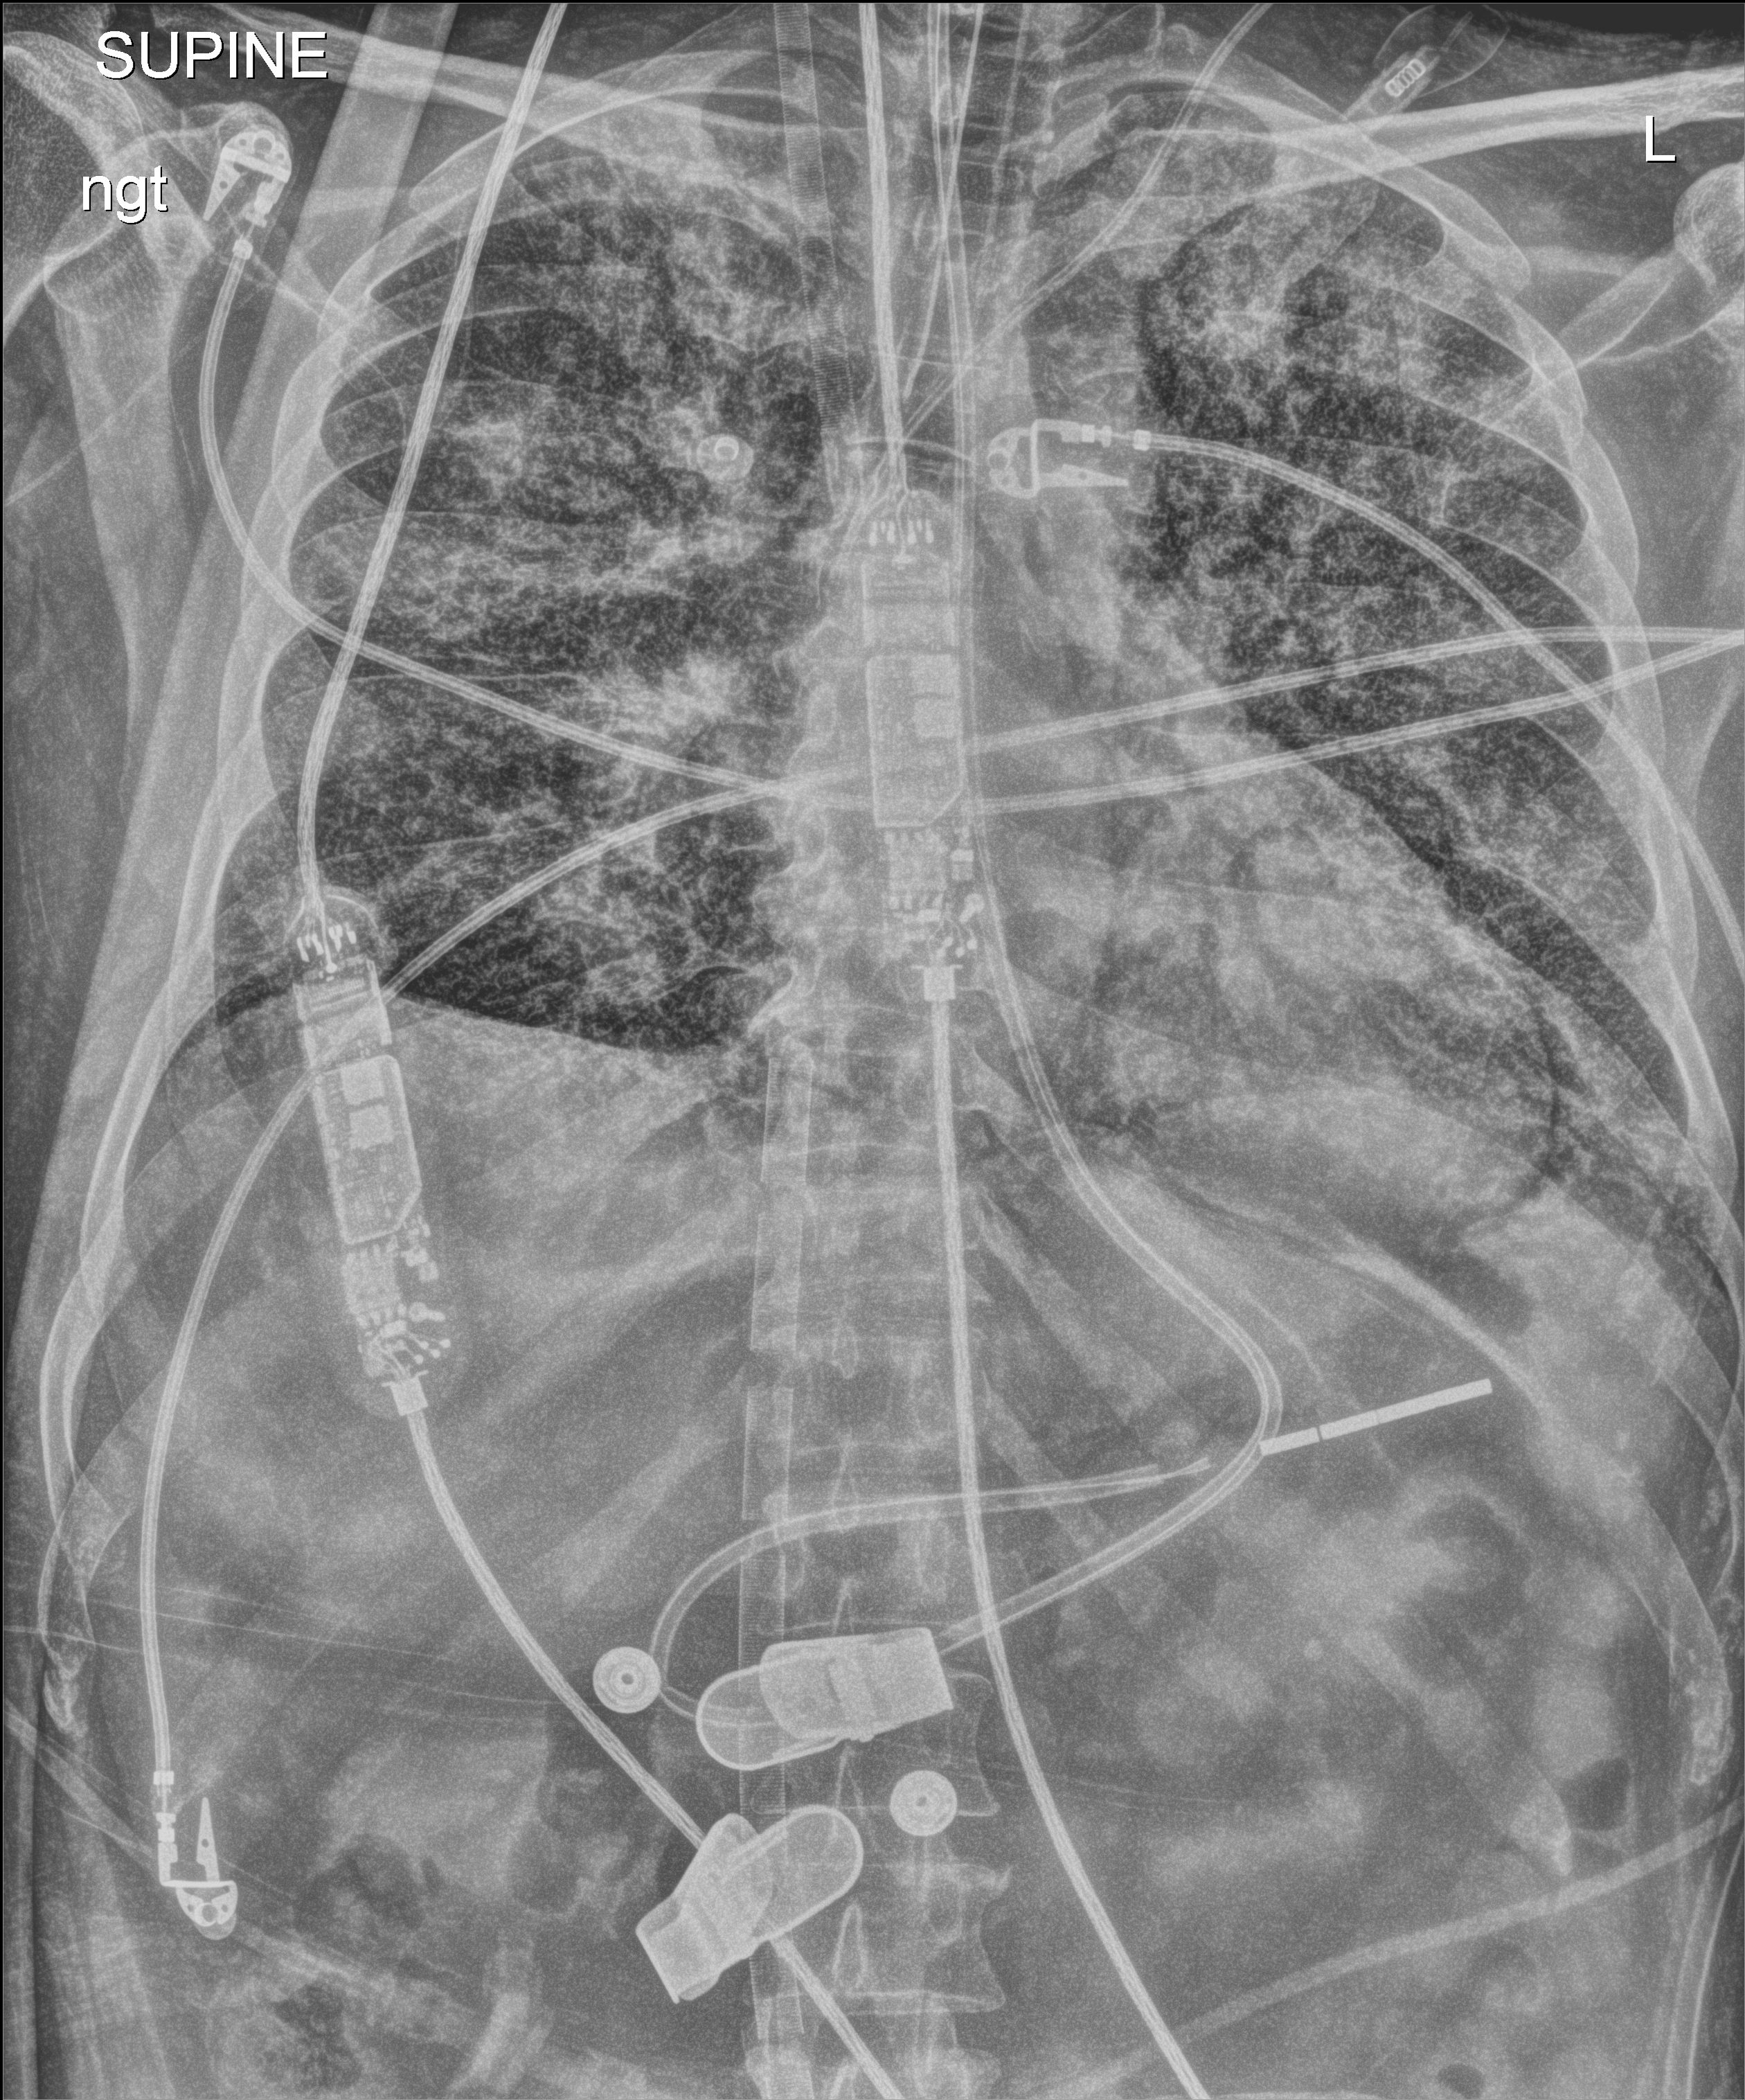
Bedside chest radiograph (digital radiography). Male patient hospitalised with COVID-19, age 18–59 years.
From the hospital-stay record, not from the radiograph (when in the stay this image was taken is not recorded):
- smoking status (admission record): never
- mechanically ventilated during this hospital stay: yes